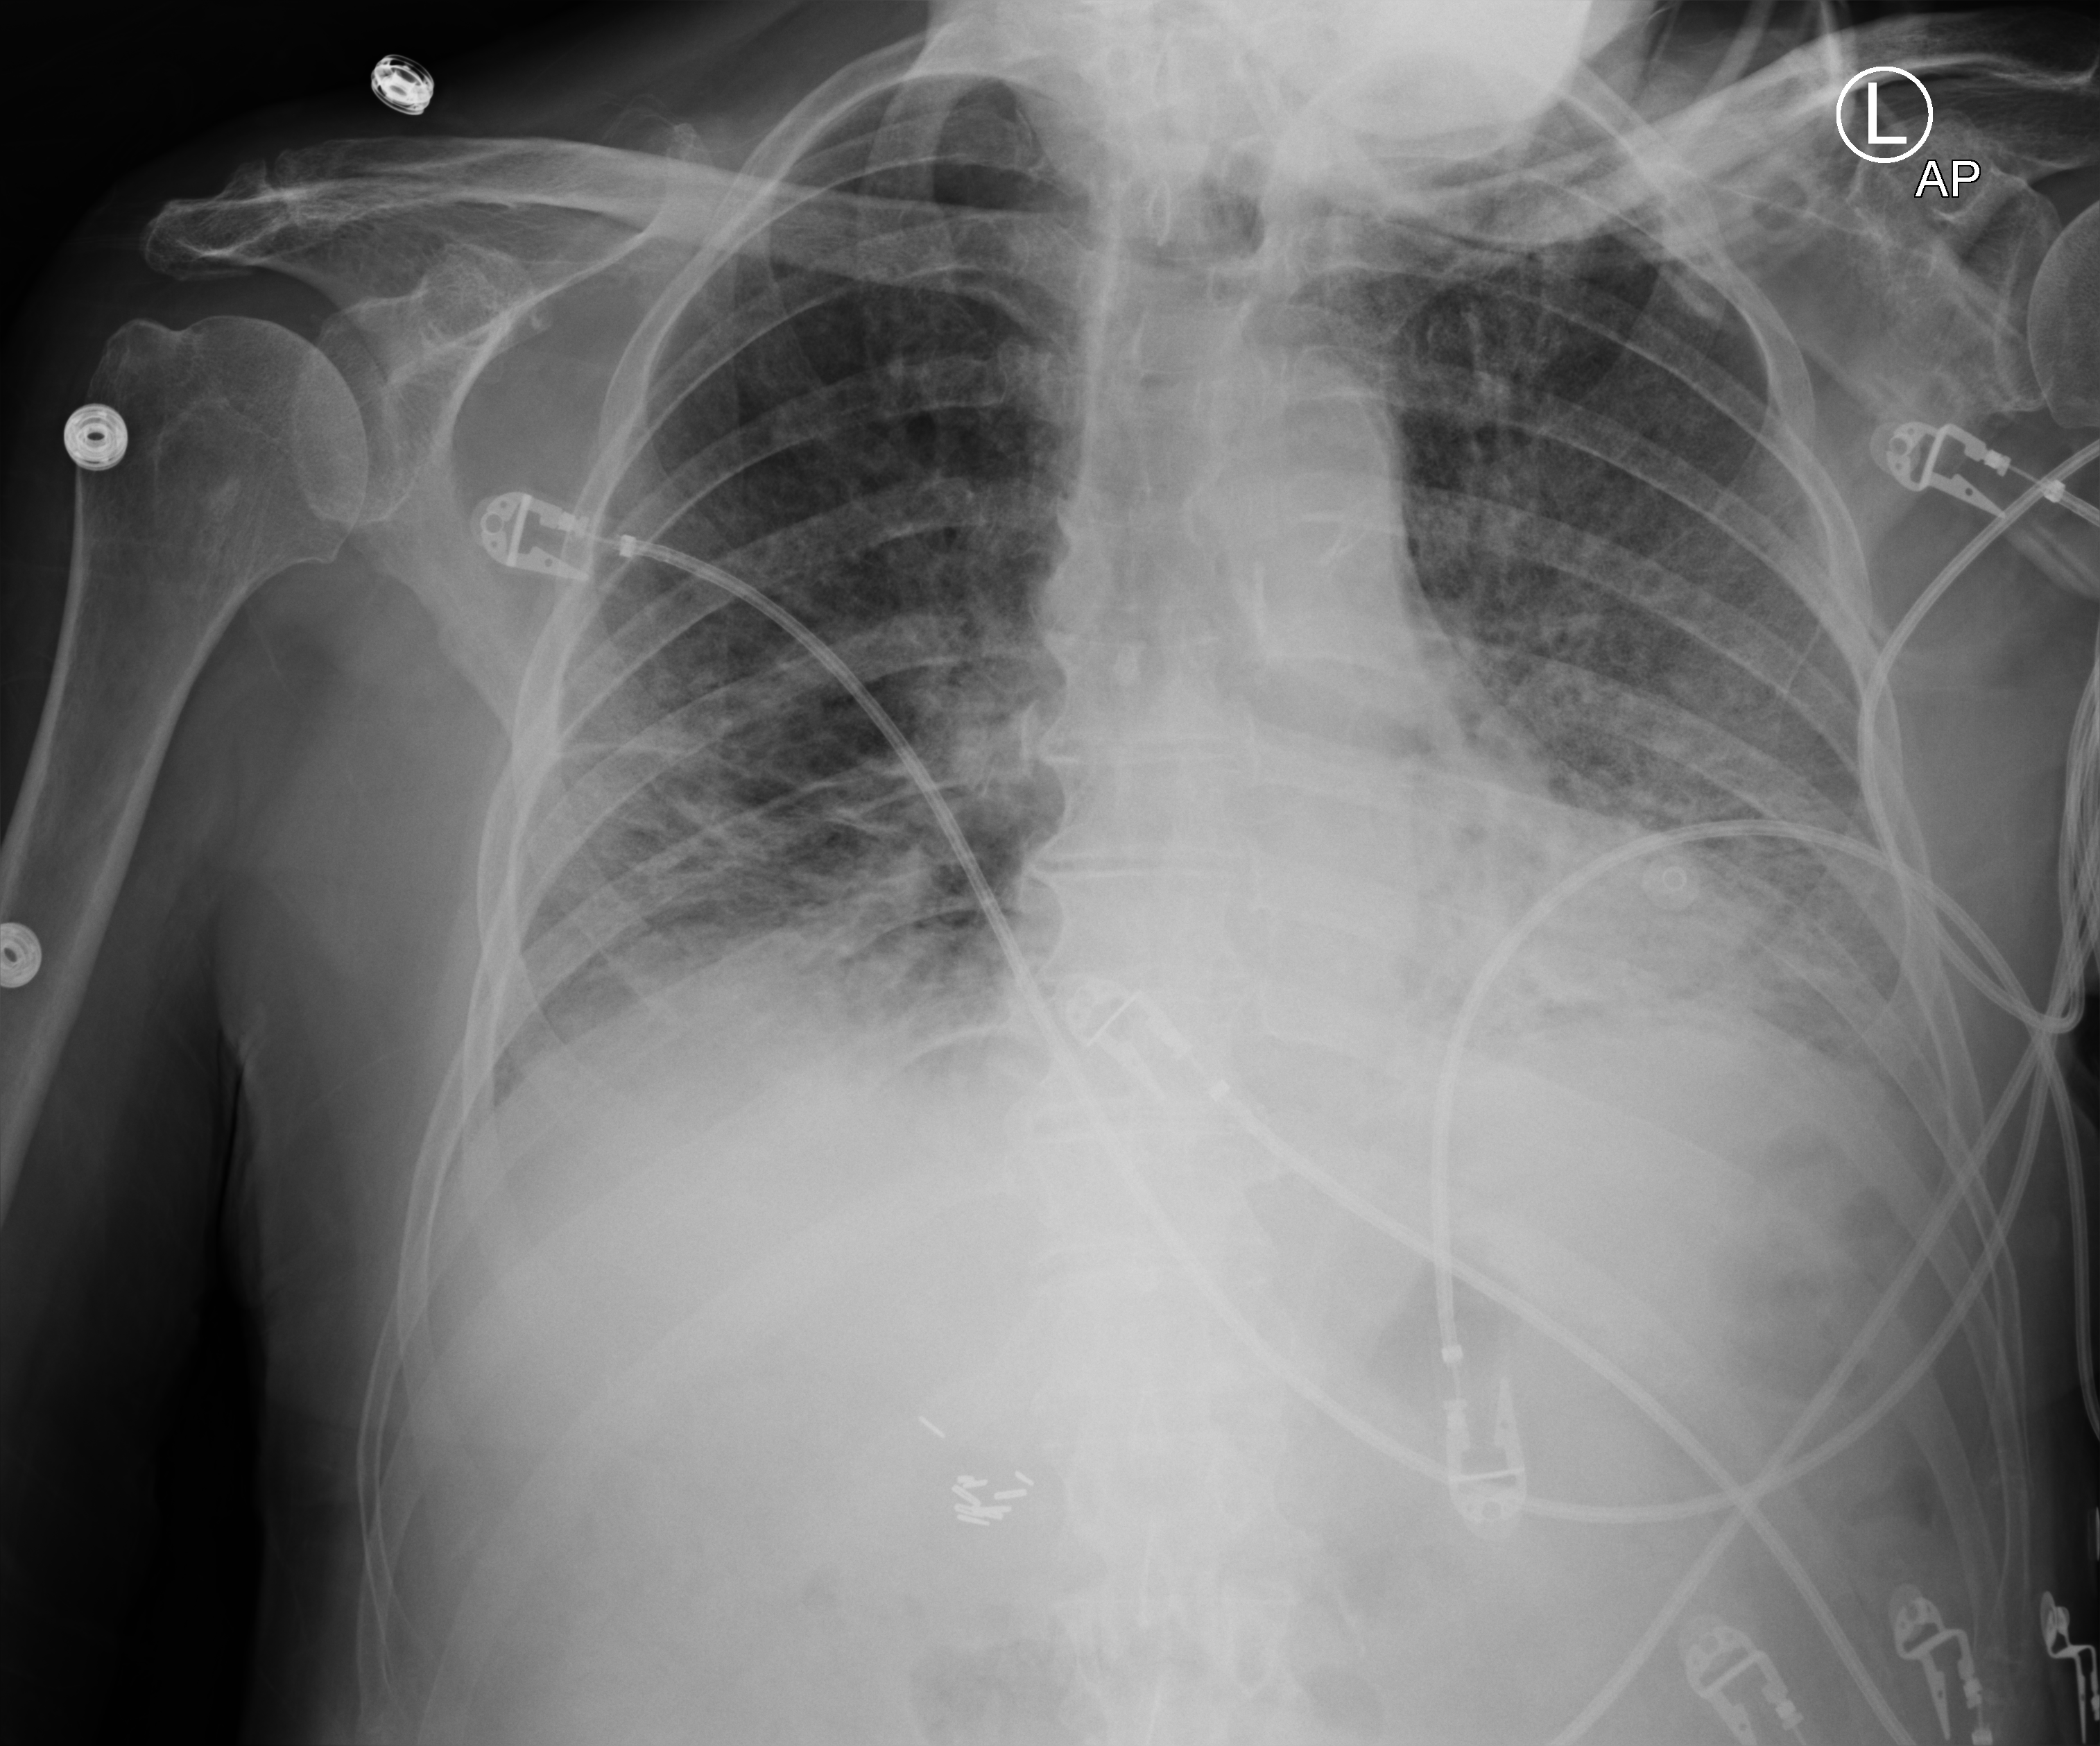
Chest X-ray (portable); anteroposterior (AP) projection. Male patient hospitalised with COVID-19, age 75–90 years.
Admission-level facts for this patient (not findings on this image; timing relative to this image not recorded):
- hypertension (admission record): yes